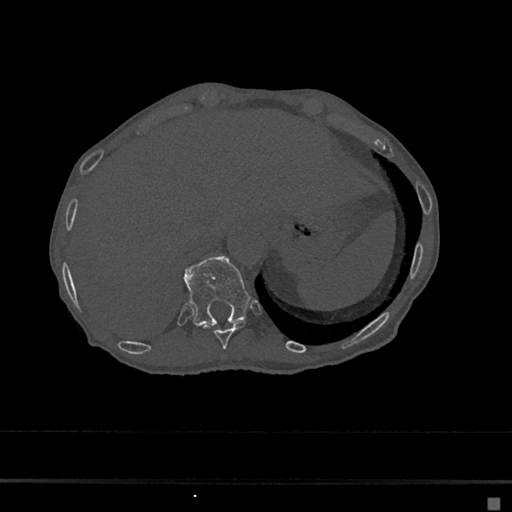
CT including the spine, one axial slice; position 193 of 797 along the scan axis; reconstruction kernel Br40s/3; 120 kVp; bone window (W 1800 / L 400 HU); 0.5 mm slice thickness; 512 × 512 image matrix, field of view 360 × 360 mm. Patient: female, 68 years. Case-level facts recorded for this patient, not image findings: primary cancer: renal.
Structures marked on this image (semi-automatically segmented with operator editing):
- T10 vertebra: bounding box <203,321,246,349> (left, top, right, bottom; pixels)
- T11 vertebra: <184,257,250,326>